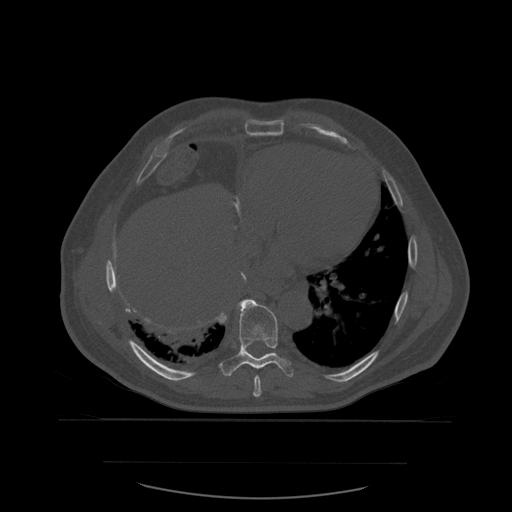
CT including the spine, one axial slice. Position 342 of 590 along the scan axis. Bone window (W 1800 / L 400 HU). 512 × 512 image matrix, field of view 479 × 479 mm. Patient age 71 years. Case-level facts recorded for this patient, not image findings: primary cancer: lung.
Outlined on this slice (semi-automatically segmented with operator editing):
- T8 vertebra: bounding box [x1, y1, x2, y2] px = [253, 376, 262, 397]
- T9 vertebra: [219, 299, 294, 378]